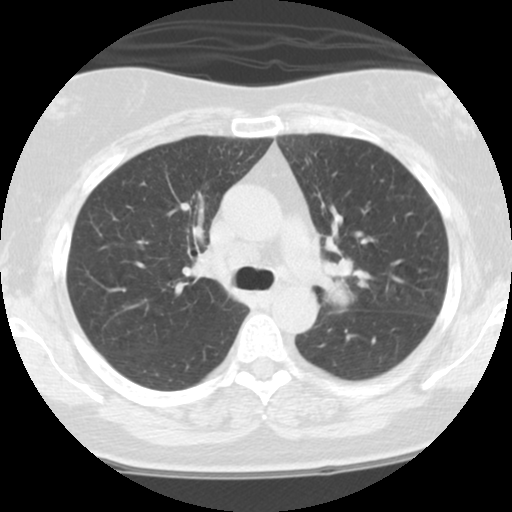
Low-dose screening chest CT, axial slice. Third screening round (two years after baseline). Lung window (W 1500 / L -600 HU). Standard (soft-tissue) reconstruction kernel (STANDARD). 120 kVp. Slice 35 of 108 in the series. Female, age 59 years at enrolment. Current smoker at enrolment.
Lesion marked by an expert reader, box from (x=284, y=212) to (x=379, y=325) px. No non-calcified nodule or mass ≥4 mm was recorded by the screening reader at this exam. Official screen result: positive, other.